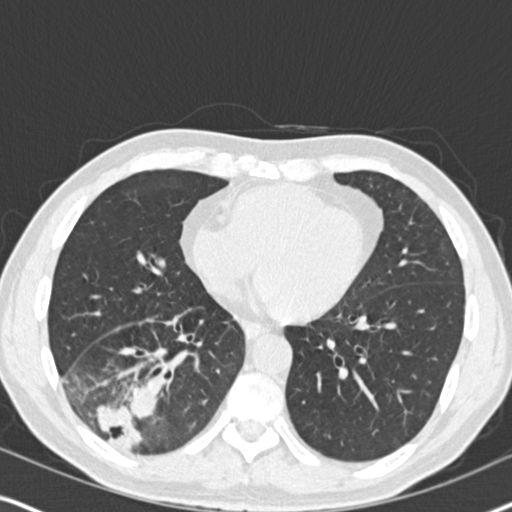
Low-dose screening chest CT, one axial slice; lung window (W 1500 / L -600 HU); 512 × 512 image matrix.
Annotated regions visible in this slice (outlined manually by an expert reader):
- lesion 1 (tumor, lower lobe of right lung): box from (x=96, y=386) to (x=158, y=448) px